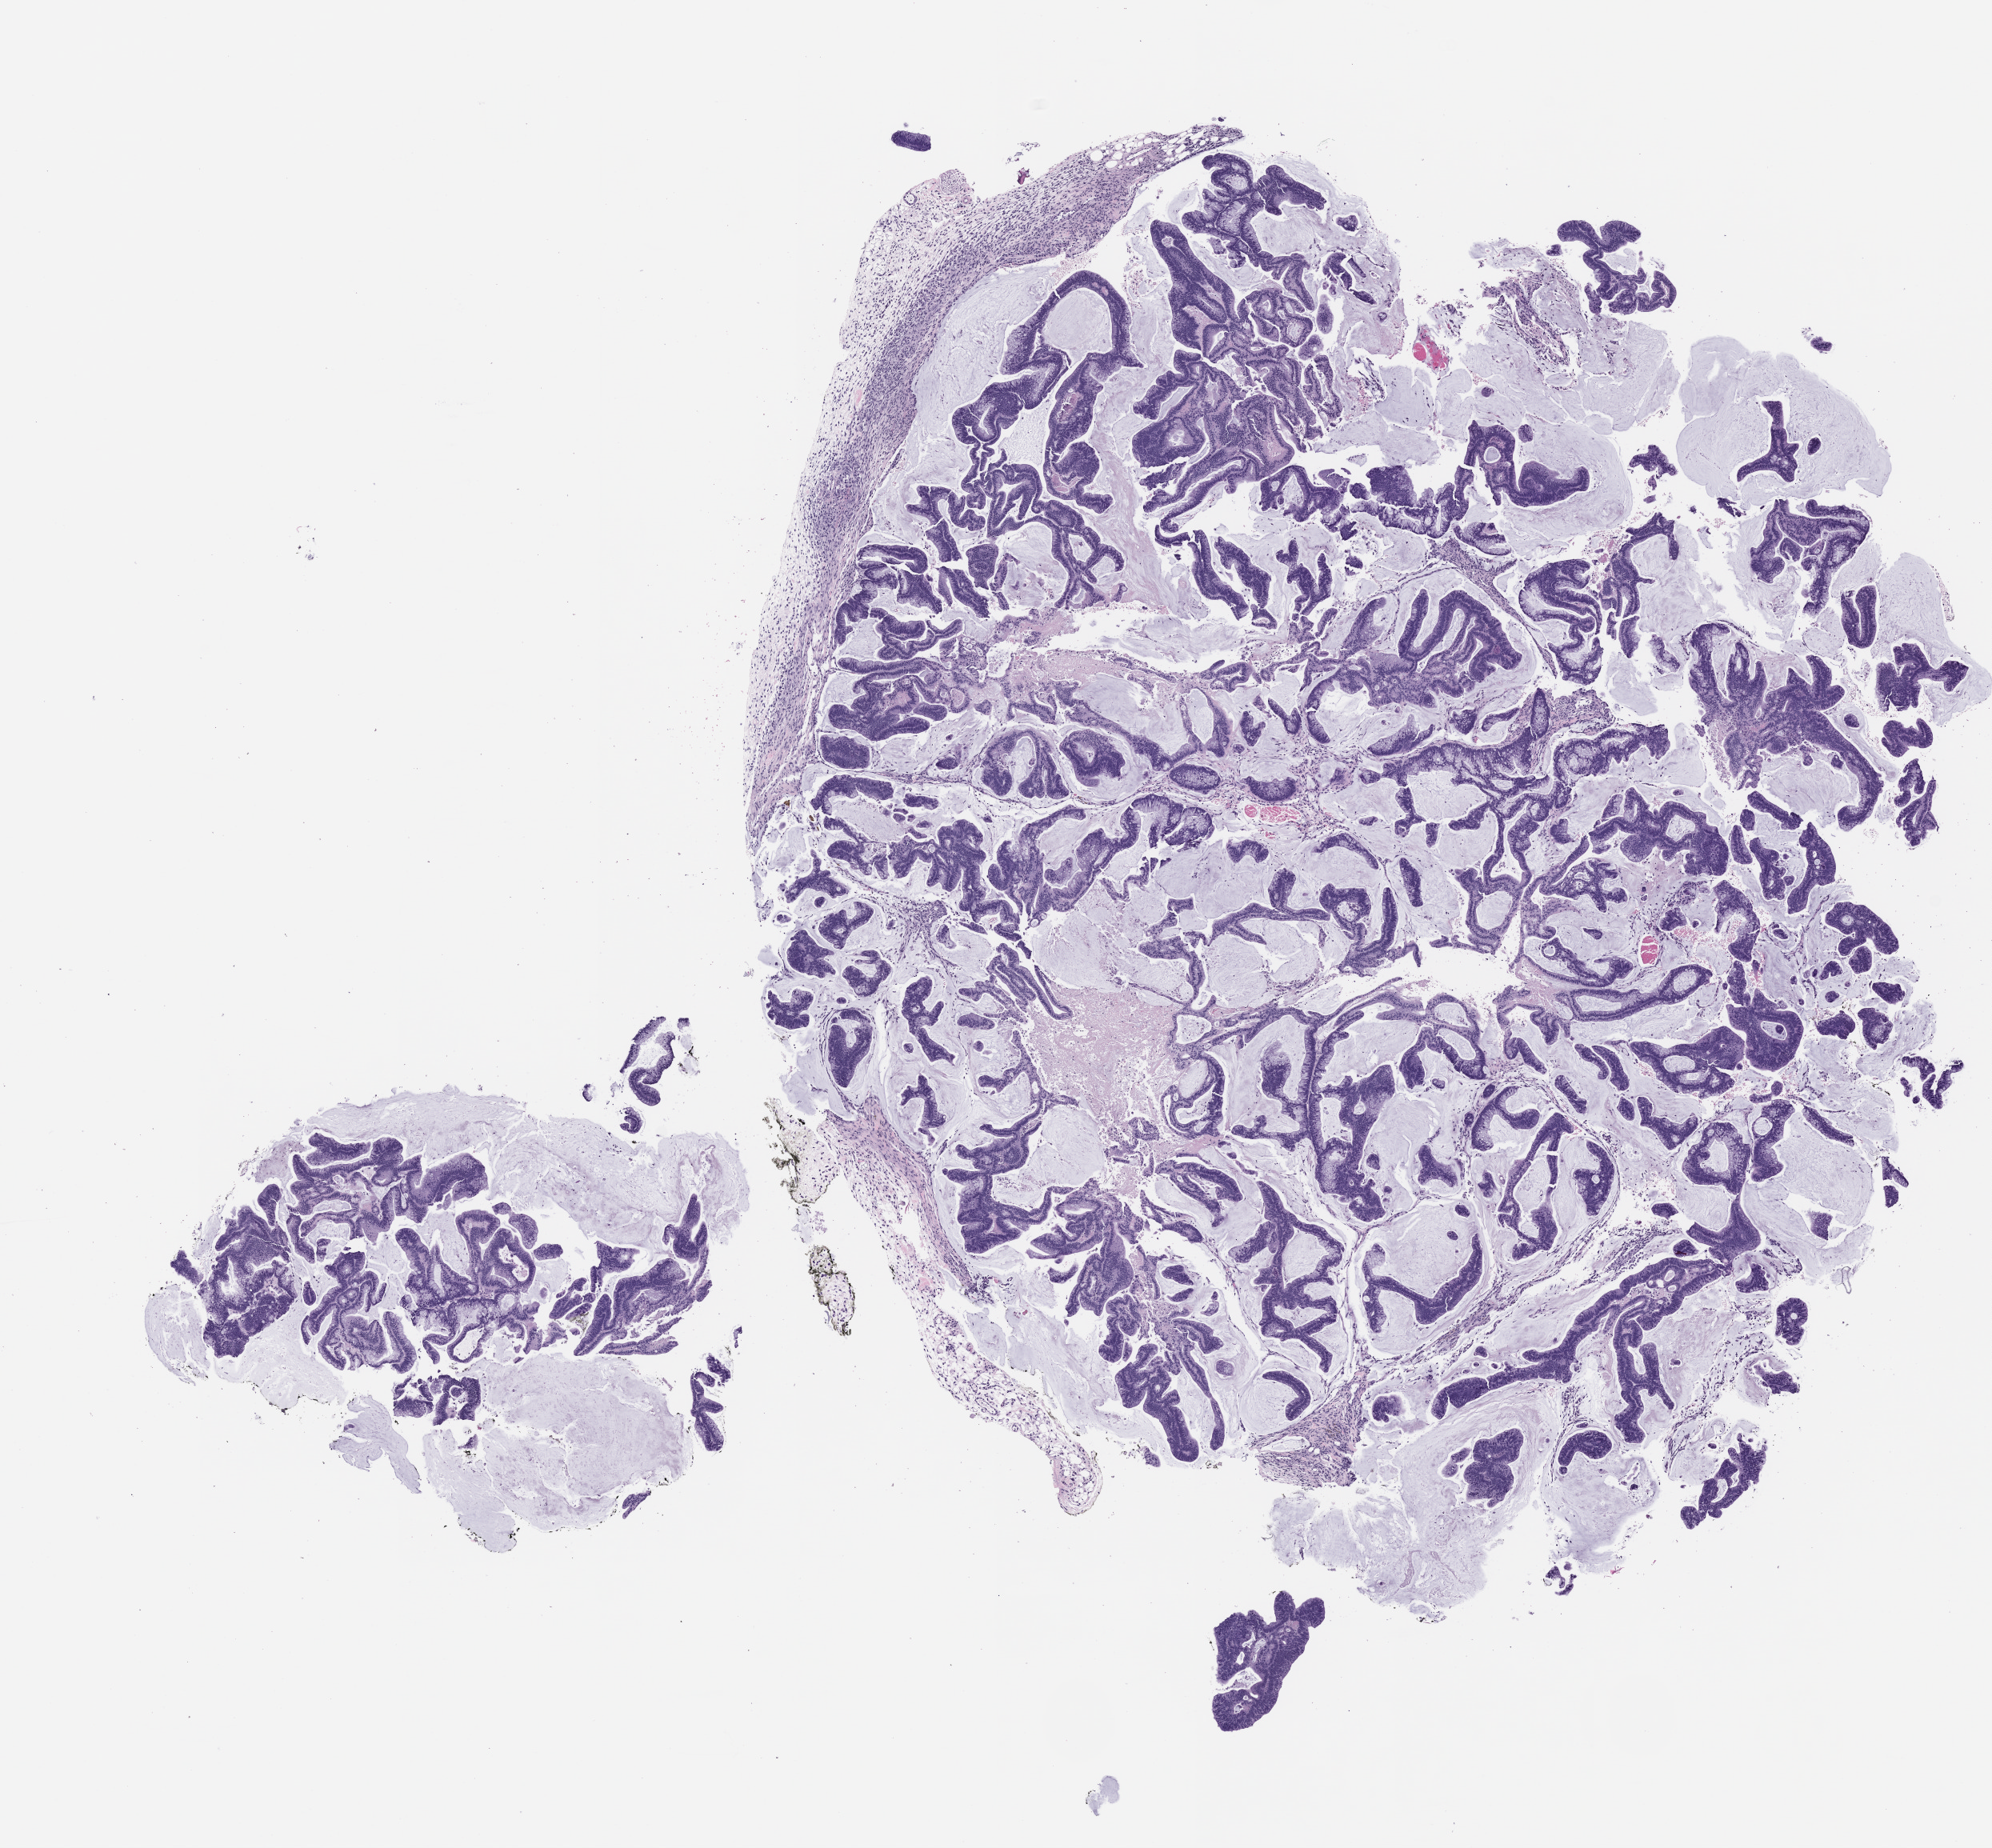
Whole-slide image, H&E: patient-derived xenograft (human tumor grown in a mouse), passage 2 — low-resolution overview of the scanned area, about 10.0 x 9.3 mm. FFPE section. Originating tumor site category: colon.
* originating patient diagnosis: Colon Adenocarcinoma